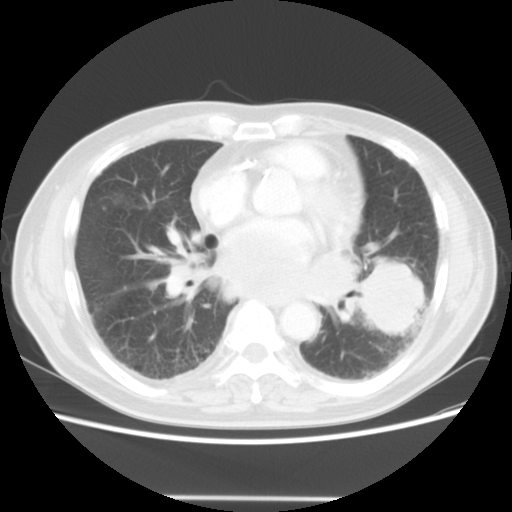
Chest CT, one axial slice. Position 22 of 56 along the scan axis. Lung window (W 1500 / L -600 HU). 5 mm slice thickness. 512 × 512 image matrix. Male patient, age 66 years. From the clinical record (not read from this slice): clinical TNM (as recorded): T4 N3 M0.
Structures marked on this image (rectangle marked by the reading radiologist):
- lung tumour (recorded histology: small cell carcinoma): bounding box (x1, y1, x2, y2) in pixels: (359, 248, 430, 344)